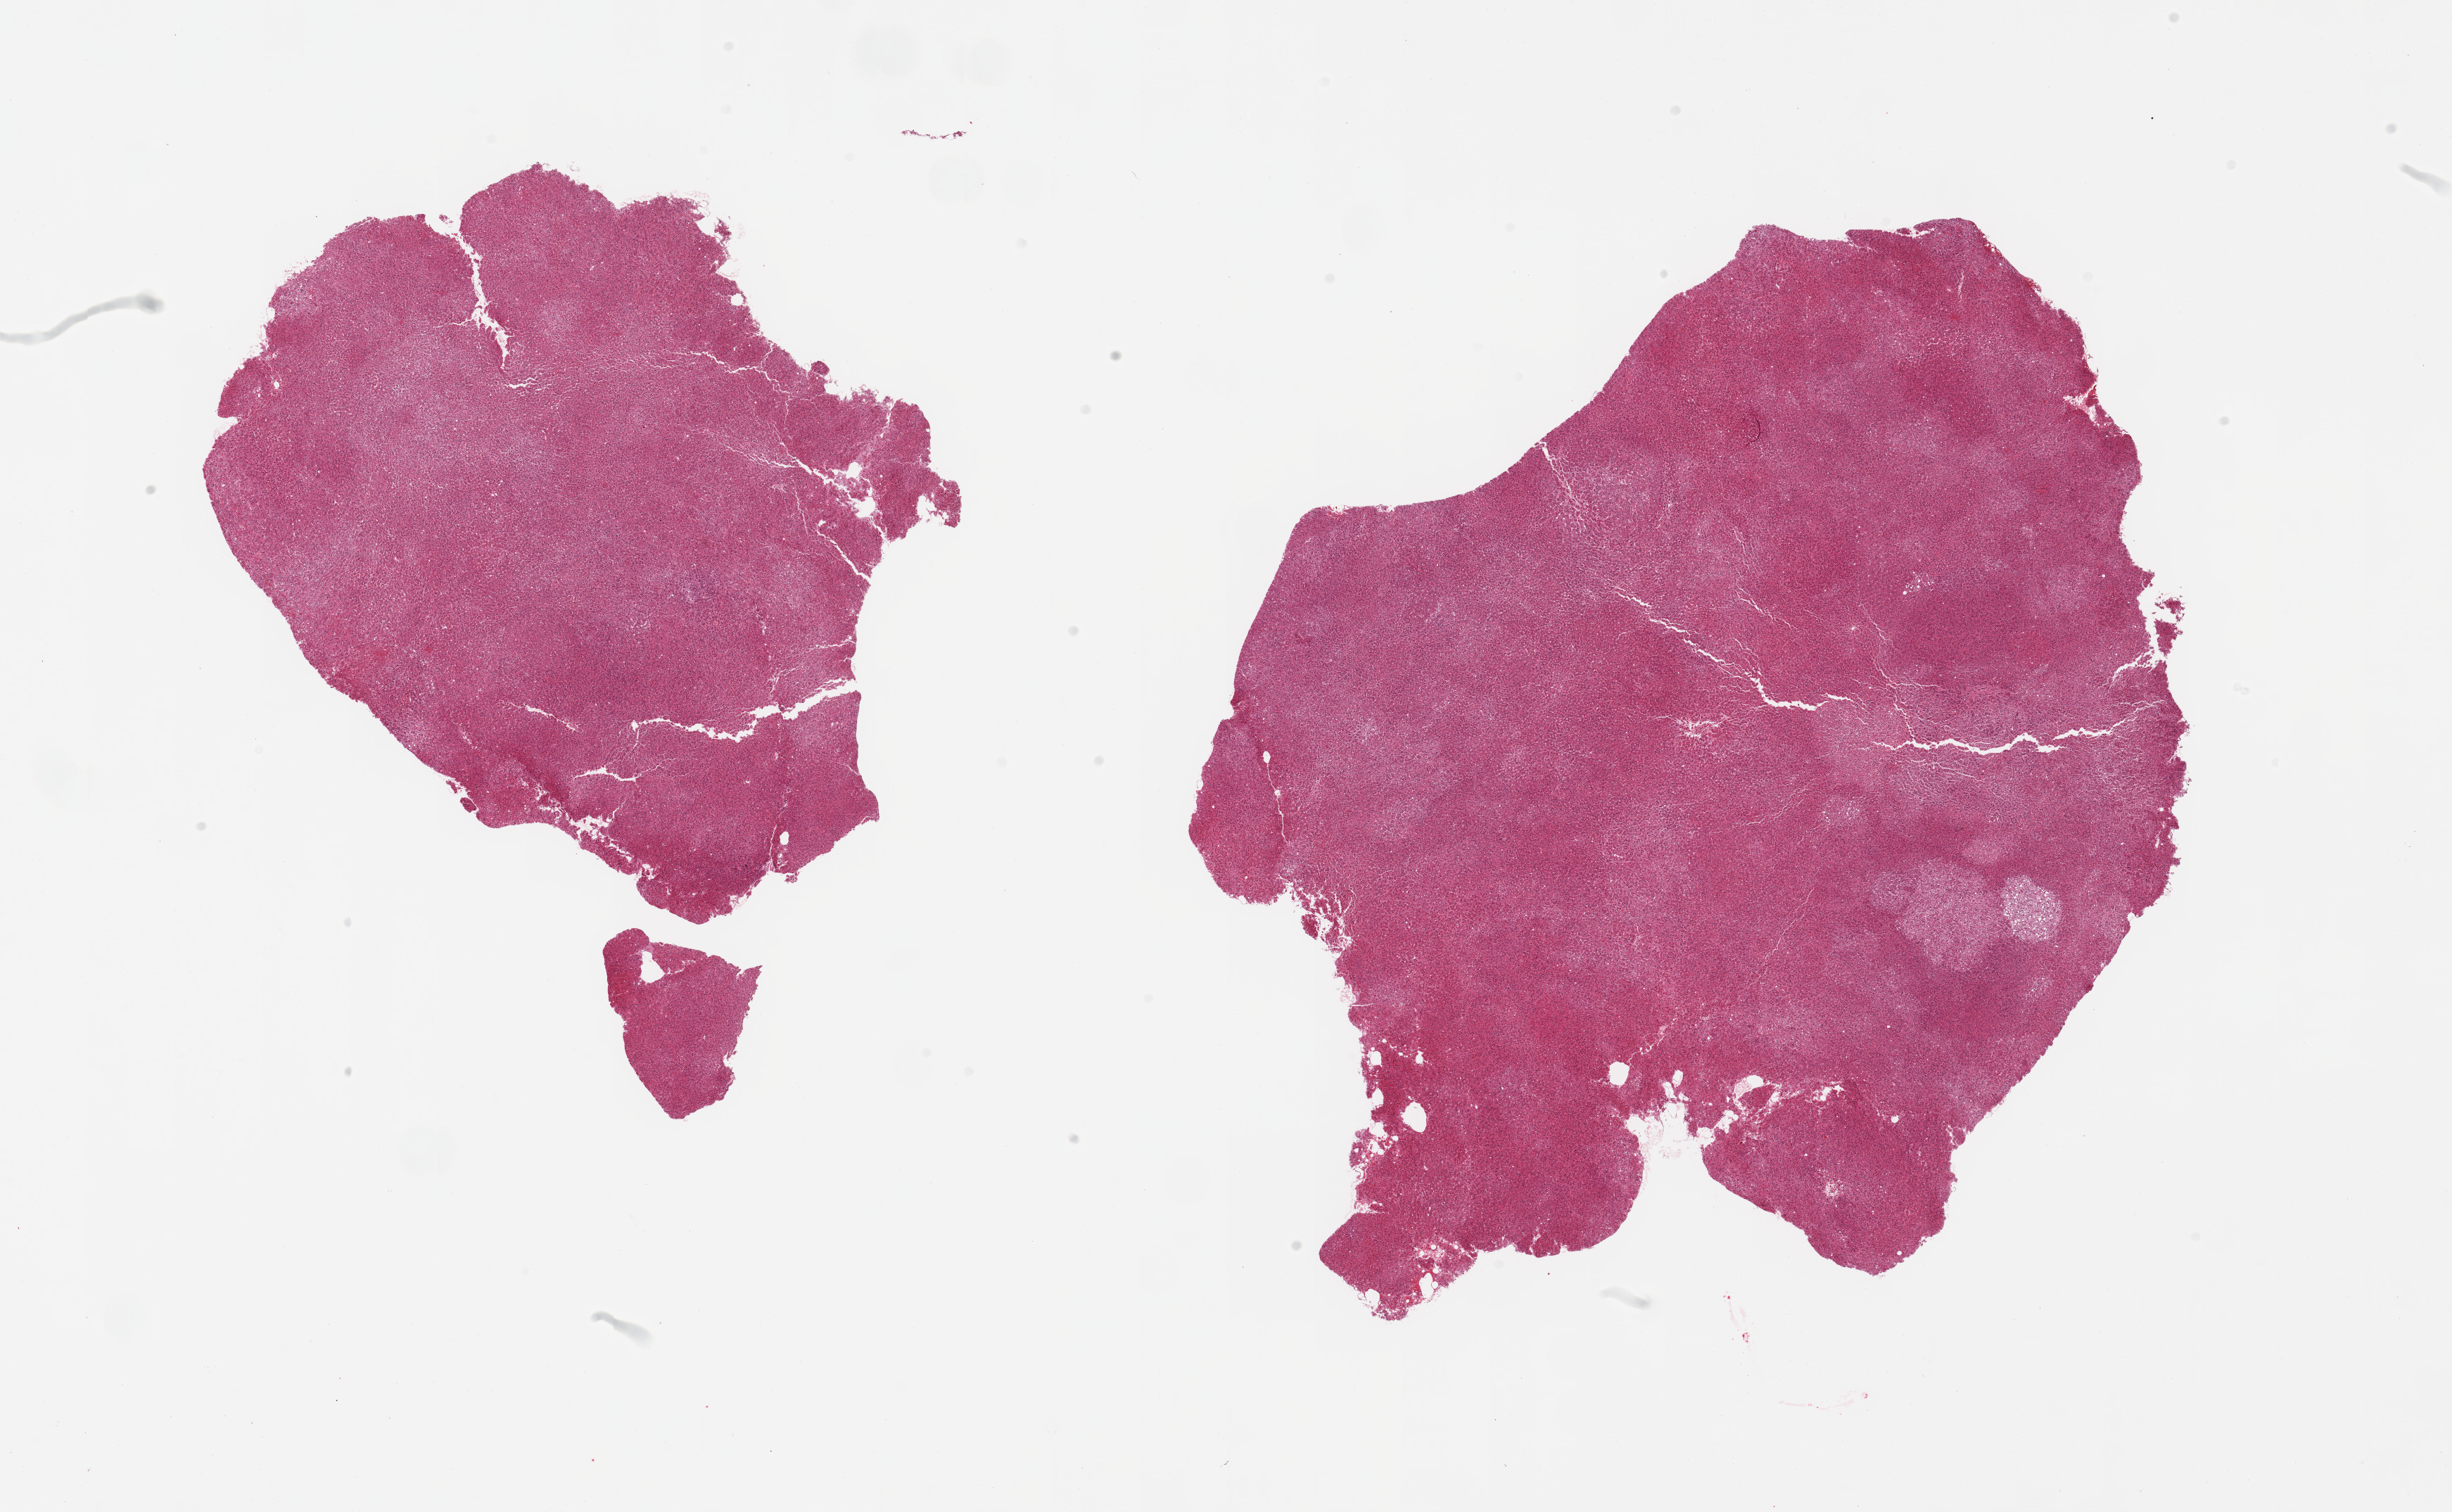
Hematoxylin and eosin (H&E) whole-slide image, brightfield, low-resolution overview of the scanned area, about 27.6 x 17.0 mm (from a 20x scan). PAXgene-fixed paraffin-embedded (PFPE) section. Section of adrenal gland (target tissue). Donor tissue sample. Donor sex: male.
• review note (as recorded): 2 pieces; mostly cortex